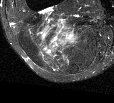
MRI of an extremity soft-tissue mass, one axial slice; slice 35 of 44 in the series (ordered by position); T2-weighted fat-saturated; MR volume resampled by the dataset authors to the PET/CT grid (not the native acquisition matrix); 3.27 mm slice thickness; 114 × 103 image matrix, field of view 111 × 101 mm. Female patient. From the clinical record (not read from this slice): histological type: liposarcoma; site of the primary tumour: right thigh.
Annotated regions visible in this slice (expert contour drawn on MRI and transferred to this co-registered scan by the dataset authors):
- gross tumour volume (mass): bounding box <54,30,80,44> (left, top, right, bottom; pixels)